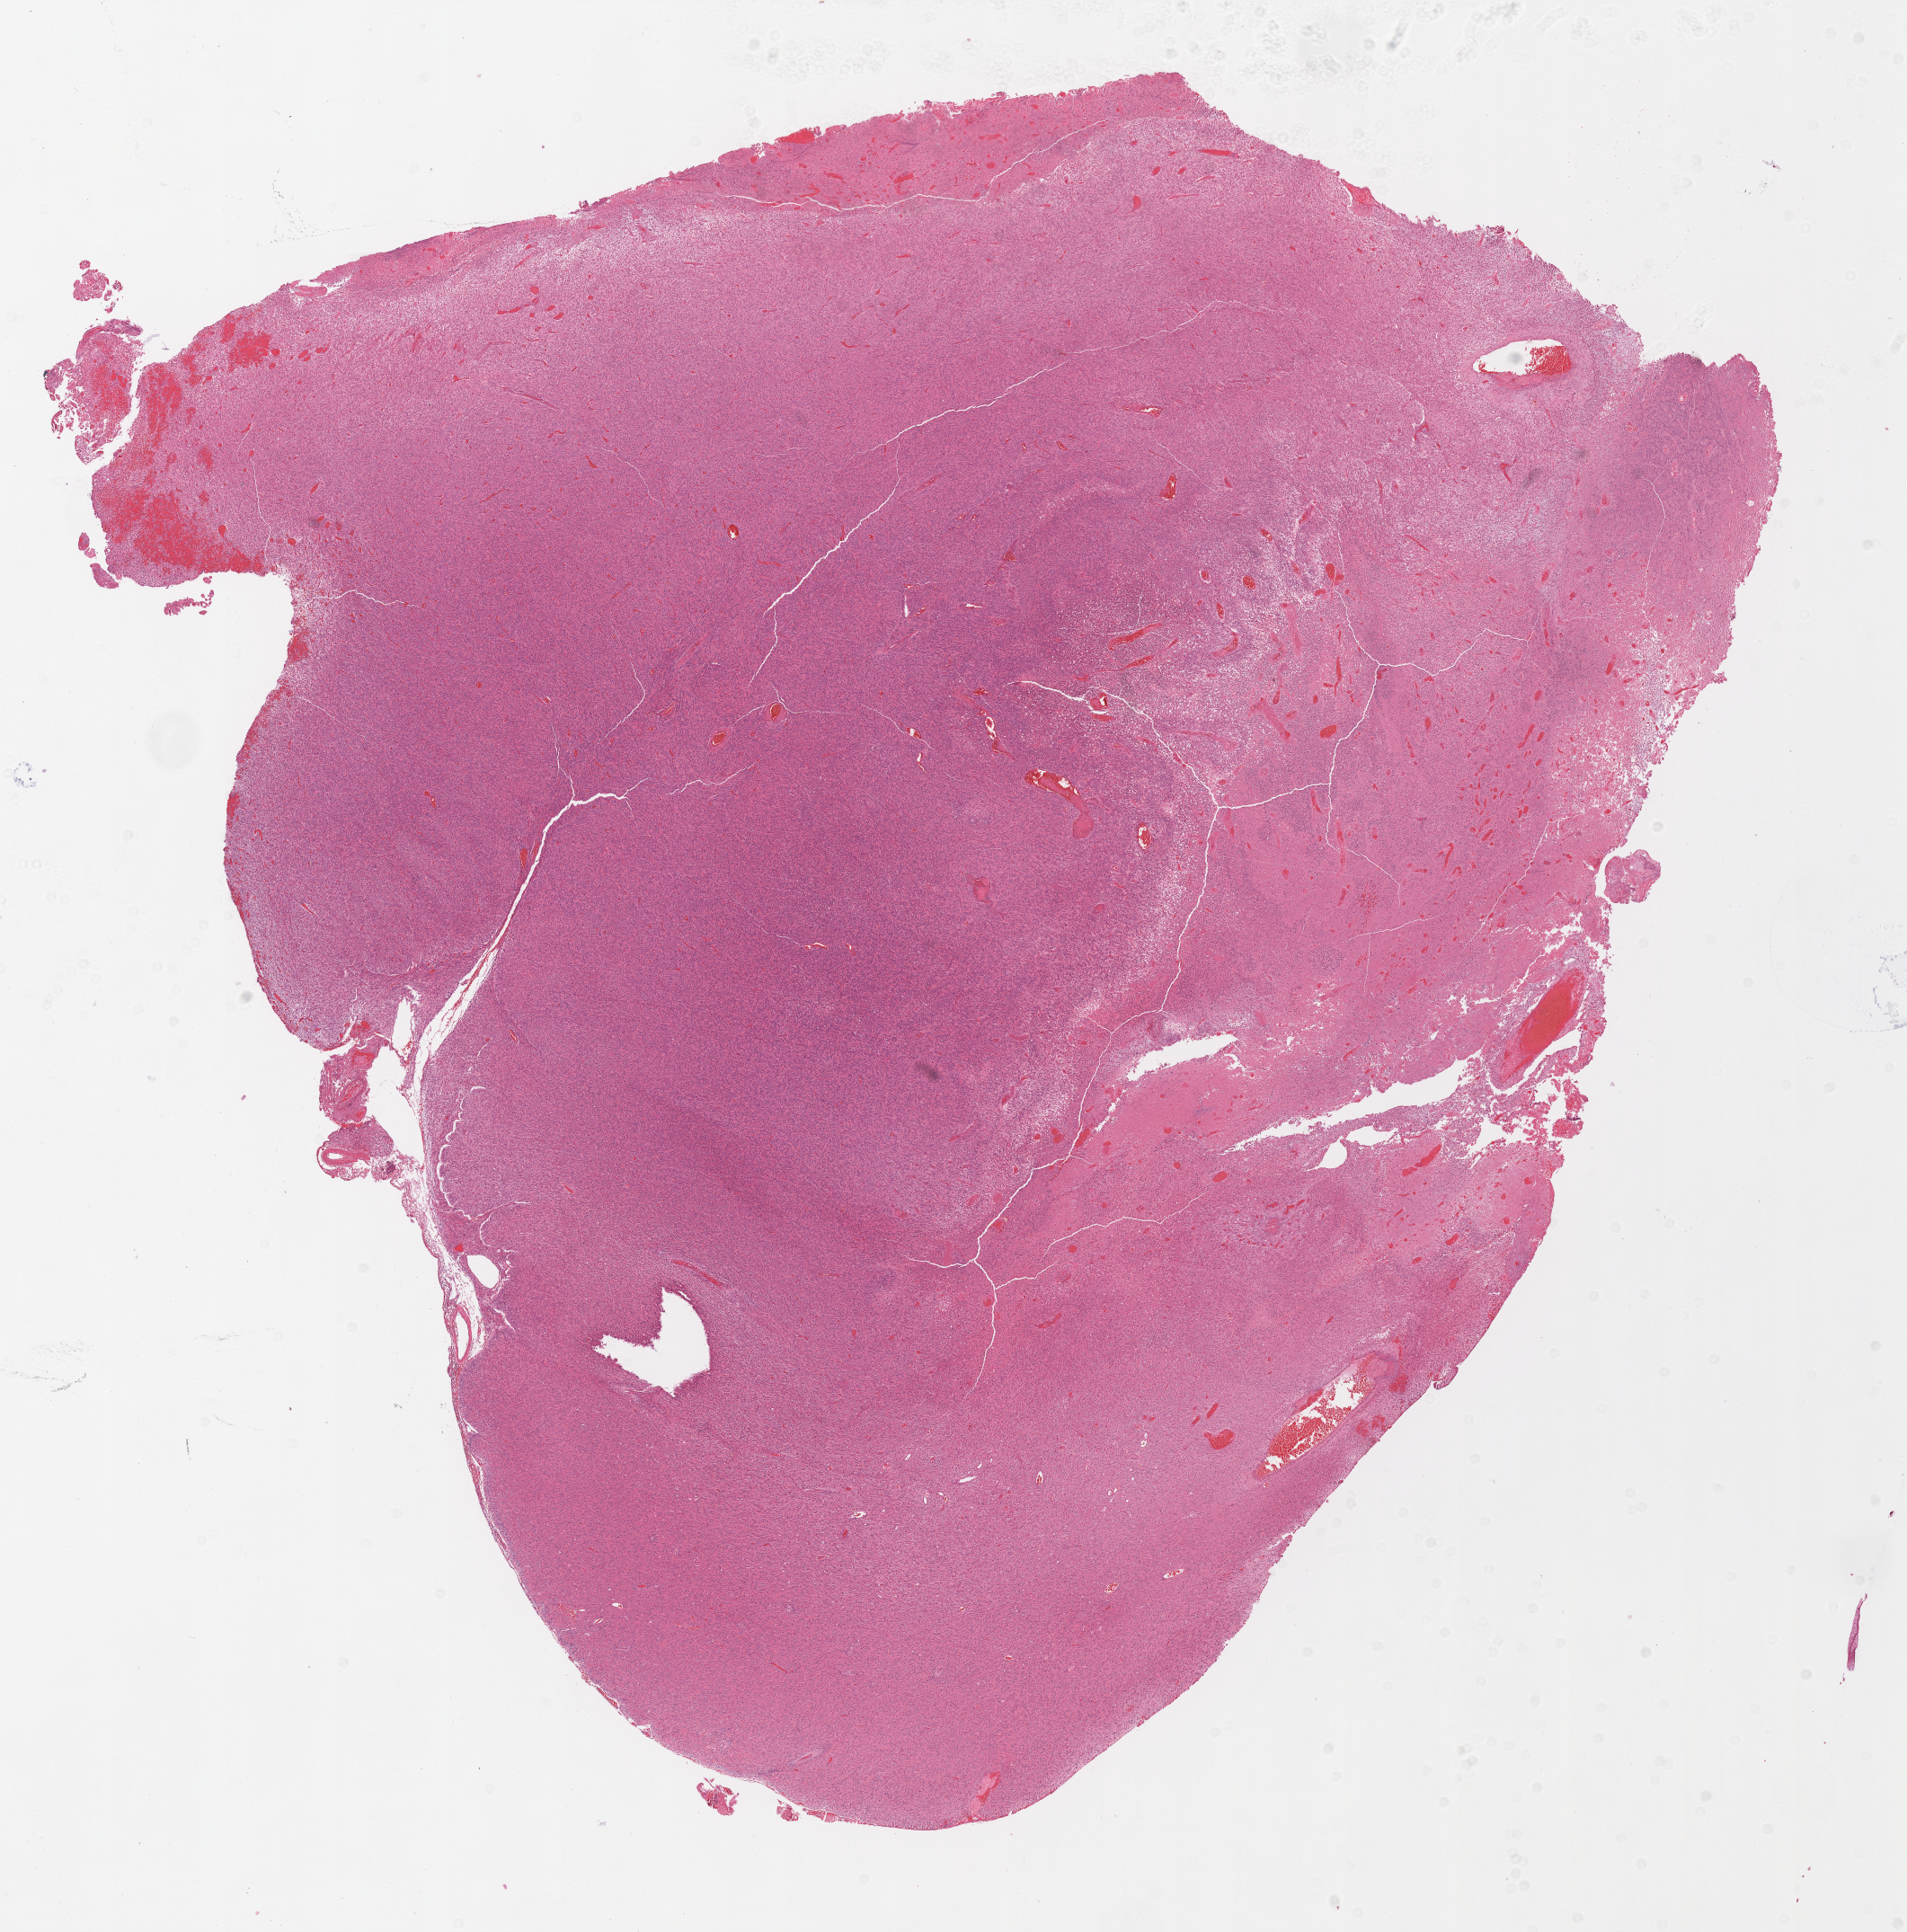
Whole-slide histology image, H&E-stained, whole scanned area (about 17.0 x 17.2 mm, acquisition: 20x scan) shown as a low-resolution overview. Formalin-fixed paraffin-embedded (FFPE) diagnostic section. Brain, primary tumour sample. Male, age 68 years at initial diagnosis.
Pathologic diagnosis: Glioblastoma.